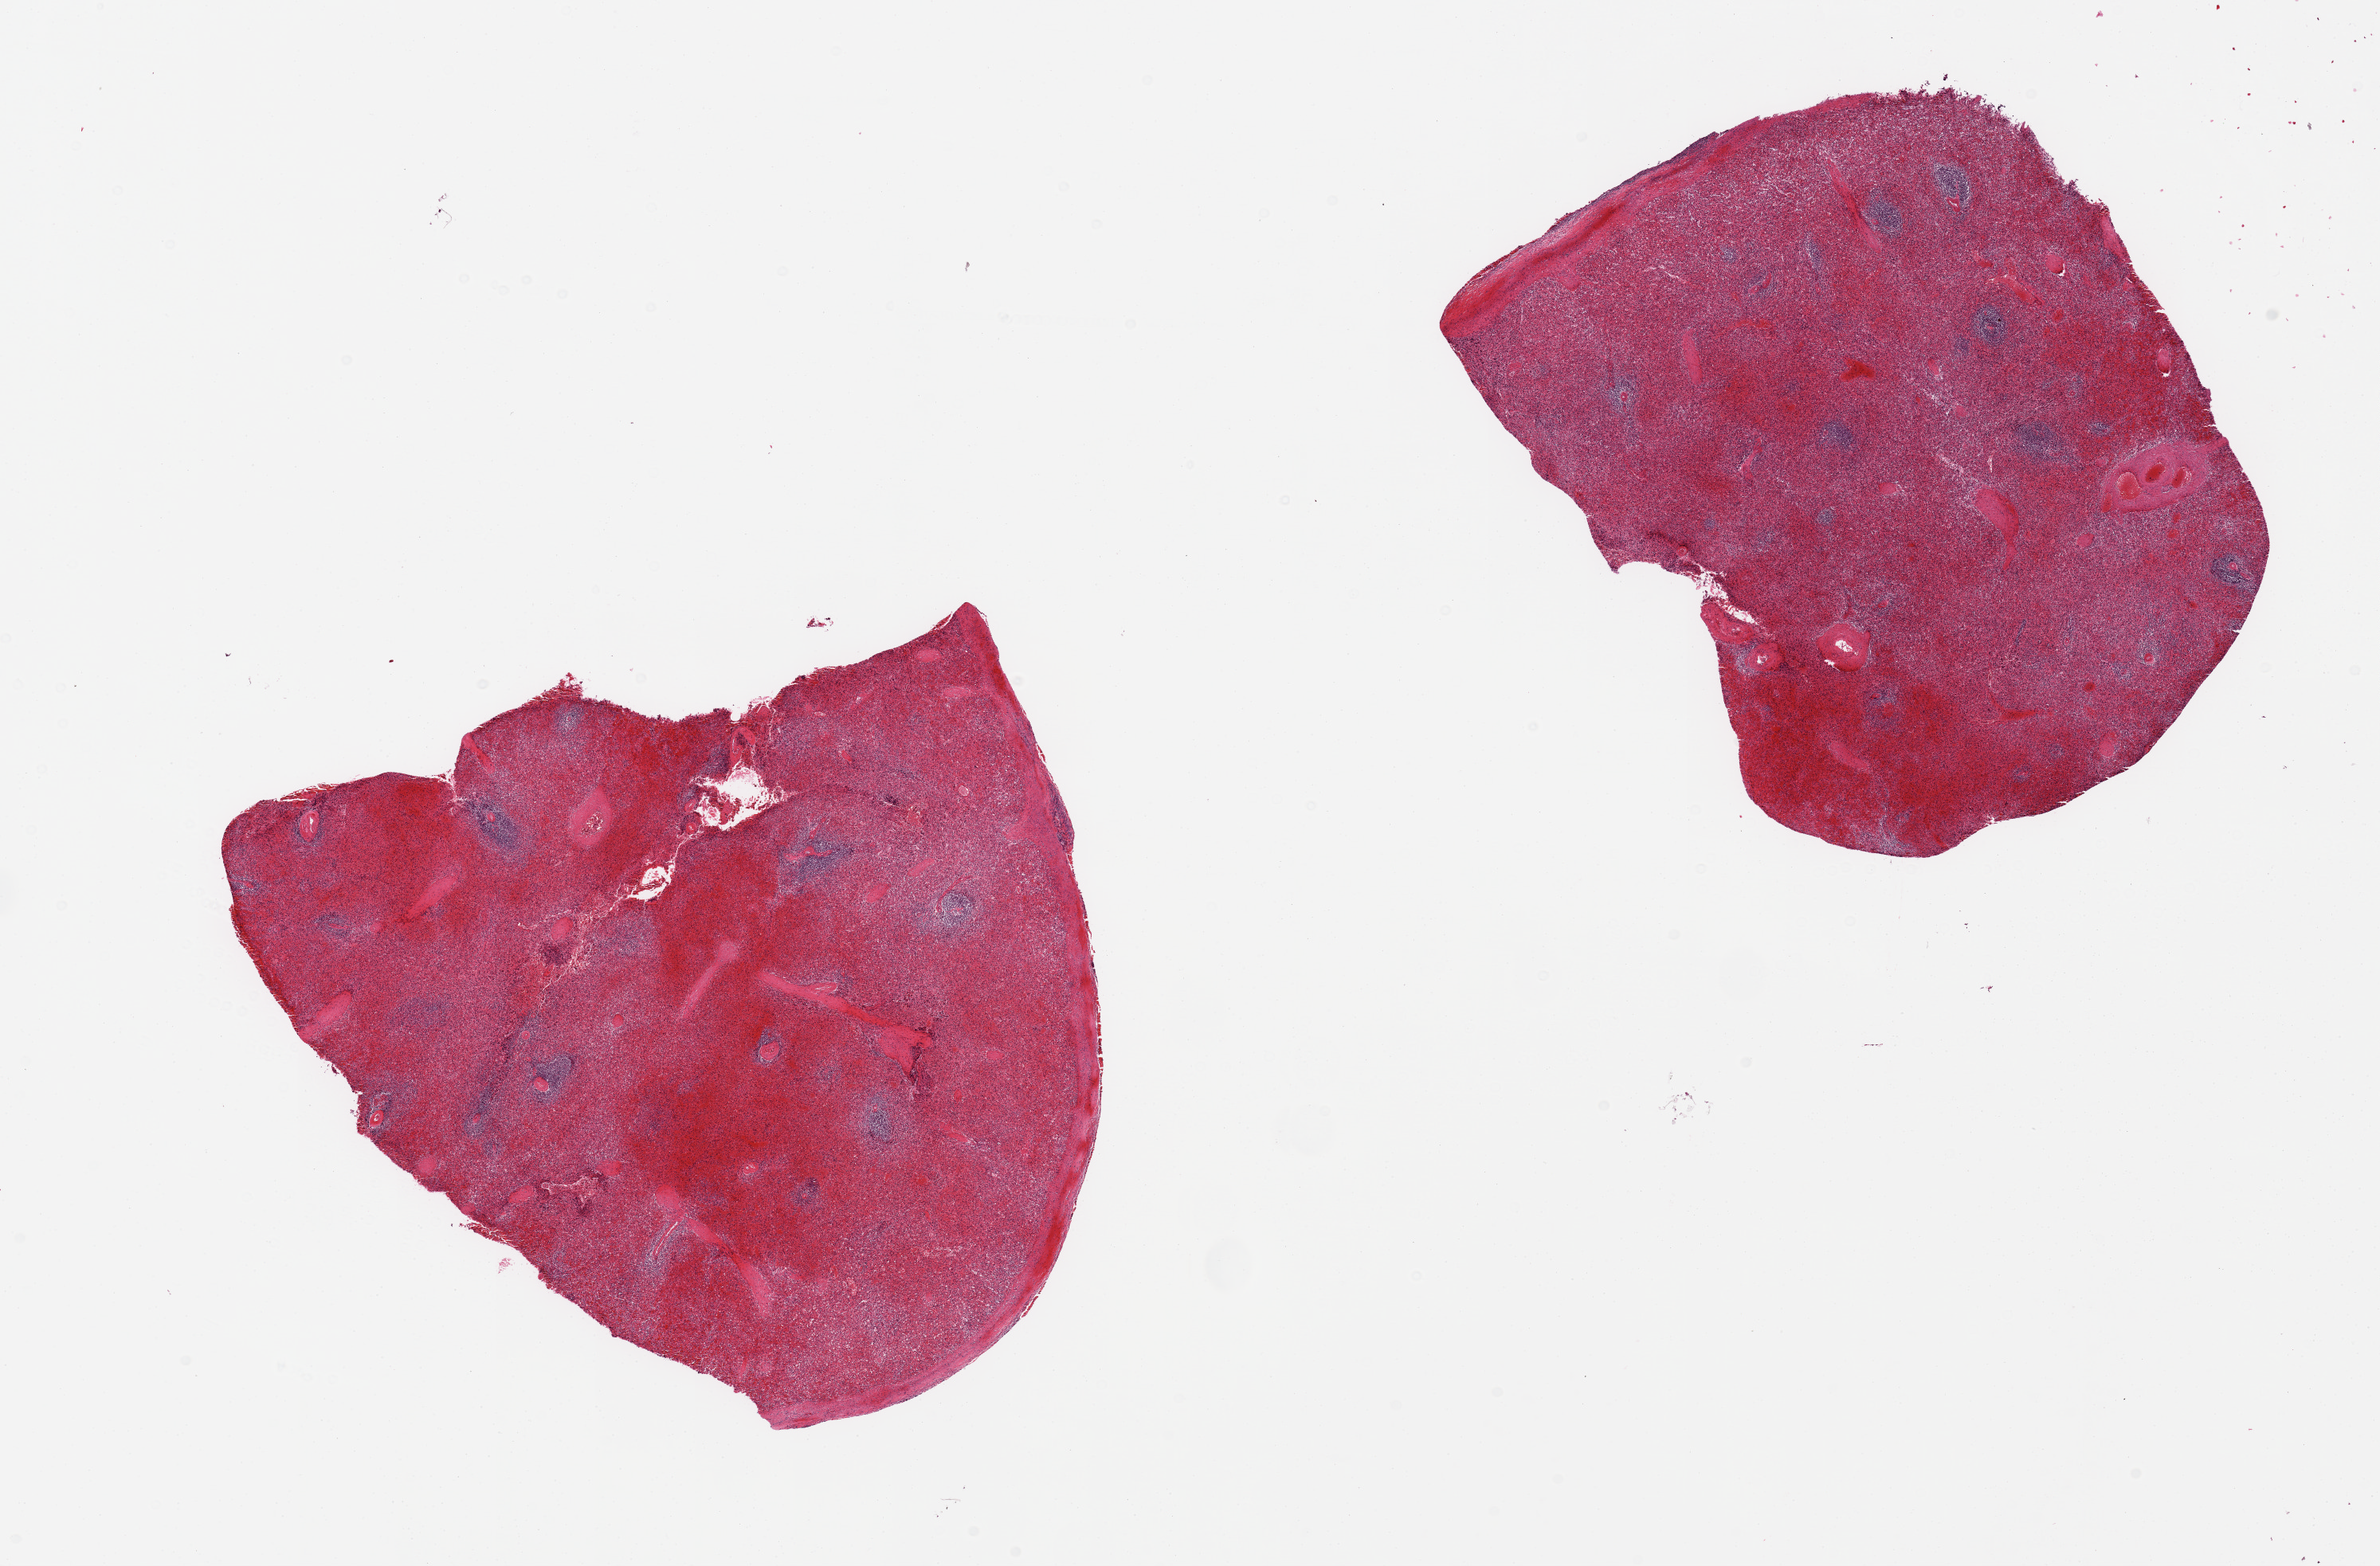
H&E whole-slide image — shown as a low-resolution overview of the whole scanned area (about 23.6 x 15.6 mm), PAXgene-fixed paraffin-embedded (PFPE) section, section of spleen (target tissue), tissue donor sample. Female donor.
Review note (as recorded): 2 pieces, marked congestion/autolysis.